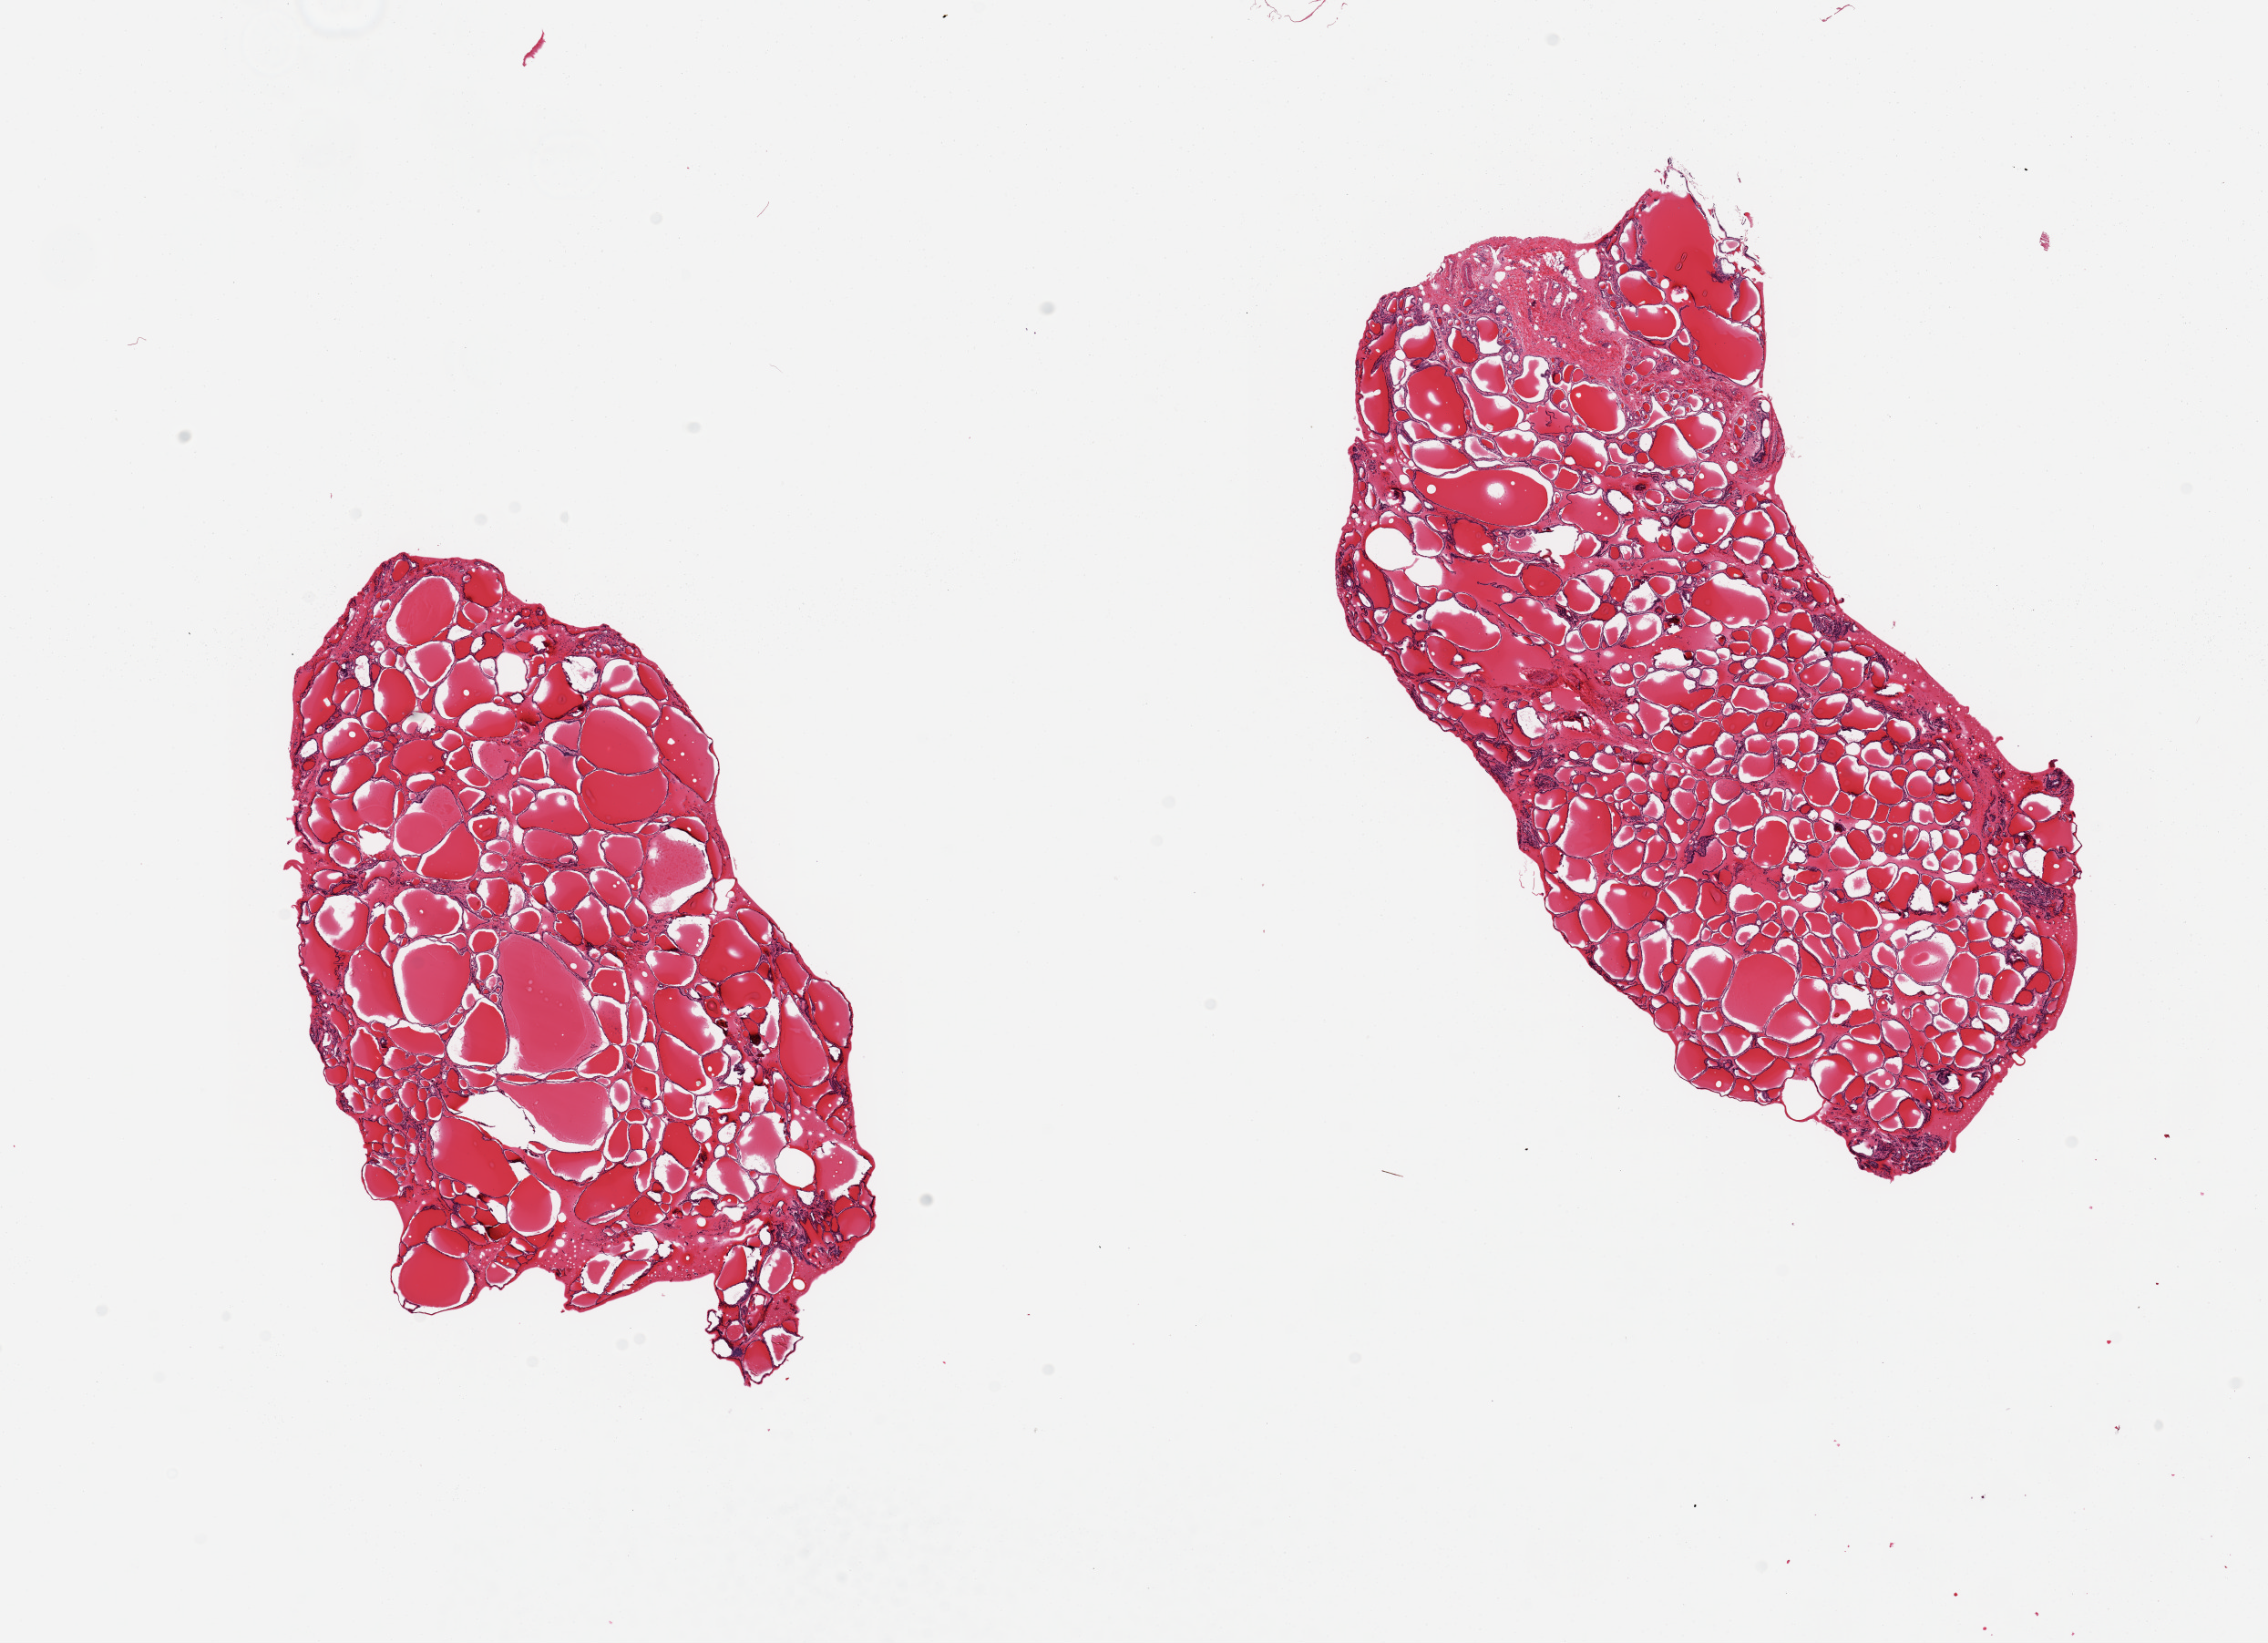
Whole-slide image, hematoxylin and eosin (H&E) stain, brightfield, low-resolution overview of the scanned area, about 19.7 x 14.3 mm, PAXgene-fixed, paraffin-embedded tissue, section of thyroid (target tissue), donor tissue sample. Donor sex: female.
Reviewer comment on this tissue sample: 2 pieces; well dissected.